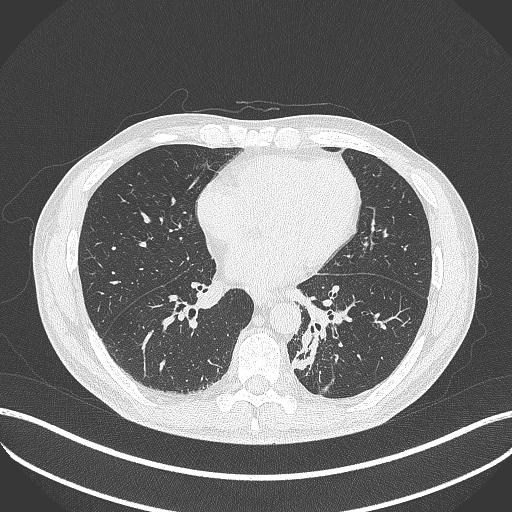
Chest CT, one axial slice. Position 164 of 451 along the scan axis. Reconstruction kernel B70f. Lung window (W 1500 / L -600 HU). 1 mm slice thickness. 512 × 512 image matrix, field of view 400 × 400 mm. Male patient, age 72 years. From the clinical record (not read from this slice): clinical TNM (as recorded): T2b N0 M1.
Structures marked on this image (rectangle marked by the reading radiologist):
- lung tumour (recorded histology: adenocarcinoma): bounding box <288,325,323,375> (left, top, right, bottom; pixels)